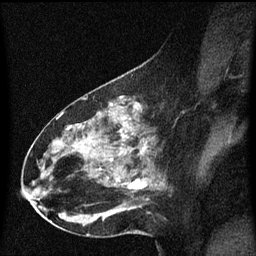
Breast MRI (dynamic contrast-enhanced), one sagittal slice; position 32 of 60 along the scan axis; dynamic contrast-enhanced series, image 2 of 3 at this slice position (ordered by acquisition); 1.5 T; TE 4.2 ms, TR 8.4 ms; 2 mm slice thickness; 256 × 256 image matrix, field of view 200 × 200 mm. Female patient, age 49 years. From the clinical record (not read from this slice): setting: breast cancer imaged before/during neoadjuvant chemotherapy; receptor status: HR-positive, HER2-negative.
Structures marked on this image (semi-automatic segmentation, software-assisted and operator-edited):
- analysis volume of interest (the breast-tissue region the enhancement analysis was run in; not a lesion): box from (x=27, y=96) to (x=168, y=221) px
- tumour enhancement mask (voxels above the 70 % enhancement threshold inside the analysis volume of interest): (x=121, y=128)–(x=147, y=181)